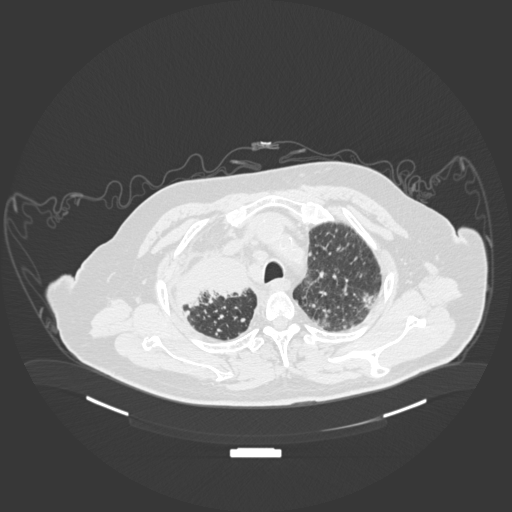
Chest CT, one axial slice. Slice 153 of 201 in the series (ordered by position). 120 kVp. Lung window (W 1500 / L -600 HU). 1 mm slice thickness. 512 × 512 image matrix. Male patient, age 69 years. From the clinical record (not read from this slice): clinical TNM (as recorded): T4 N3 M1.
Outlined on this slice (rectangle marked by the reading radiologist):
- lung tumour (recorded histology: adenocarcinoma): box from (x=172, y=249) to (x=251, y=314) px